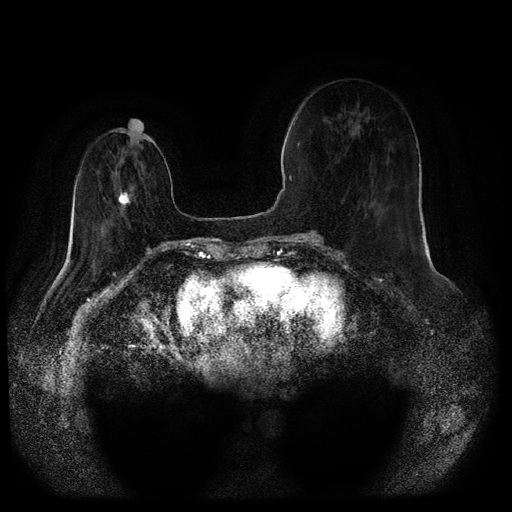
Breast MRI (dynamic contrast-enhanced, multi-phase), one axial slice; slice 28 of 116 in the series (ordered by position); dynamic contrast-enhanced series, time point 2 of 5 at this slice position (early post-contrast); 1.5 T; TE 2.6 ms, TR 5.3 ms; 2 mm slice thickness; 512 × 512 image matrix. Patient: female, 71 years.
Outlined on this slice (semi-automatic segmentation, software-assisted and operator-edited):
- breast lesion (labelled 'tumour' in the annotation; benign lesions carry a separate 'benign' label): bounding box (x1, y1, x2, y2) in pixels: (118, 191, 132, 207)